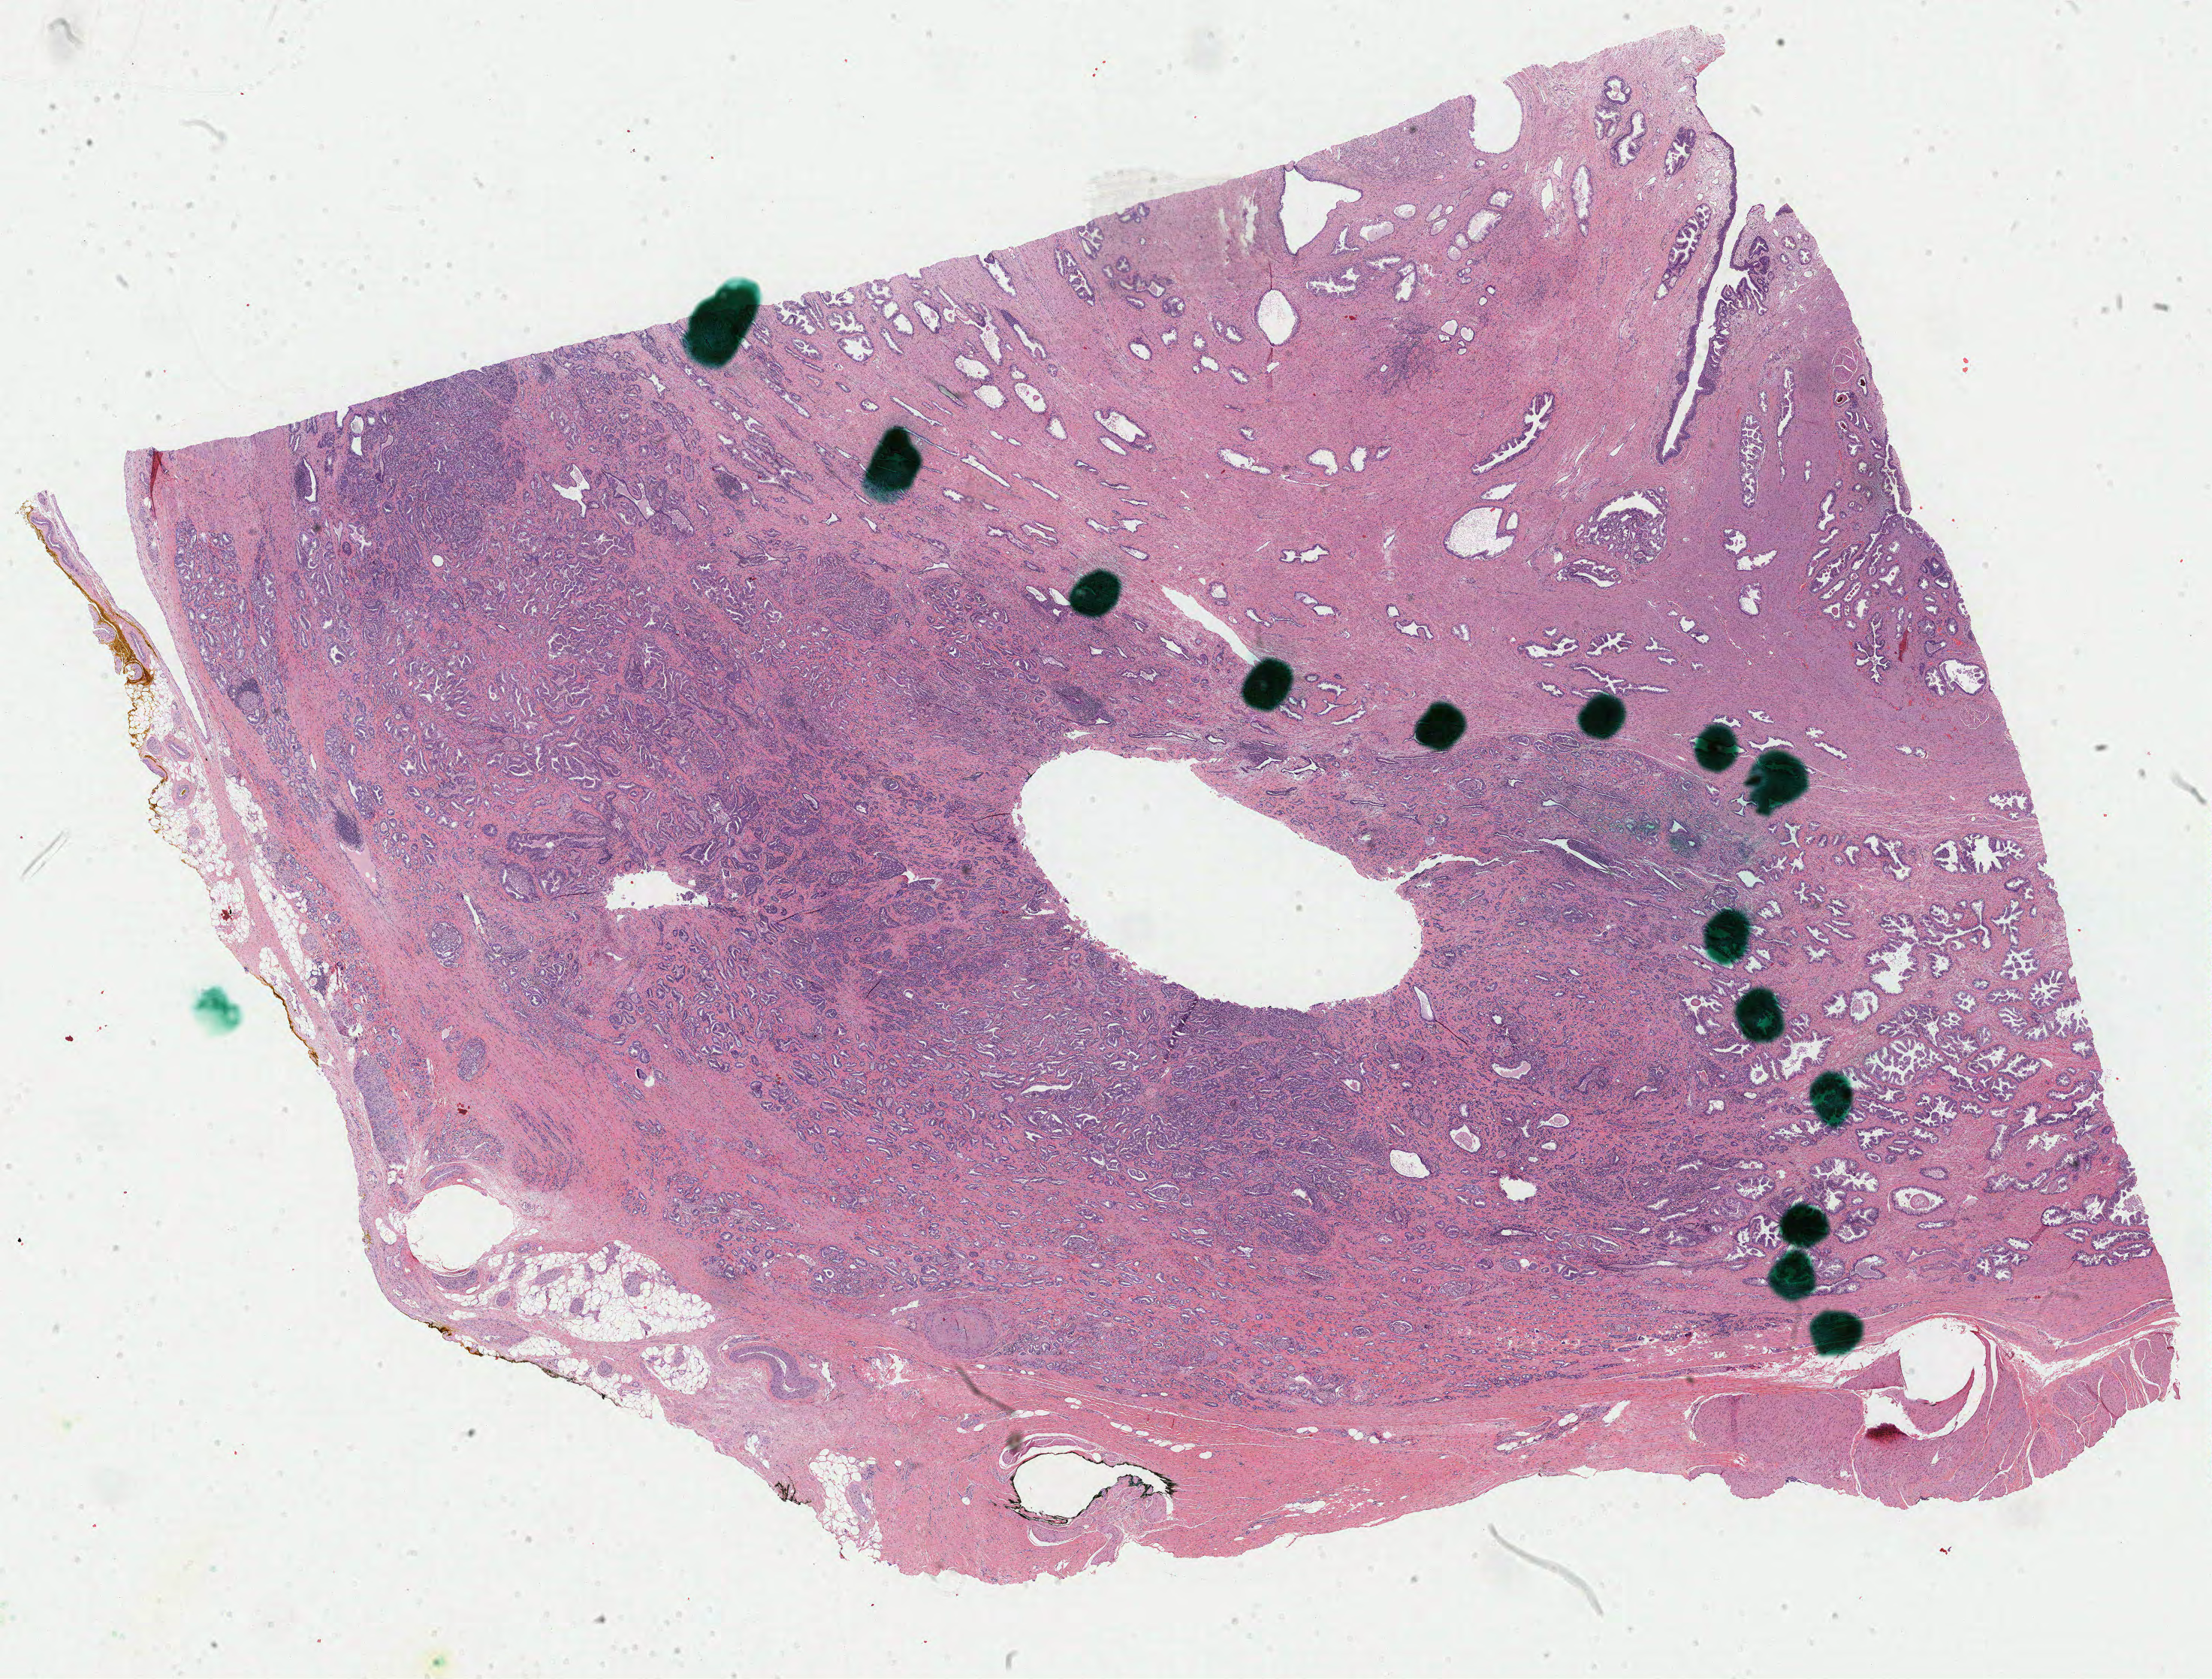
Hematoxylin and eosin (H&E) stained whole-slide image, low-resolution overview of the scanned area, about 23.4 x 17.7 mm (from a 40x scan), formalin-fixed paraffin-embedded (FFPE) diagnostic section, primary tumour sample from the prostate. Male patient; age at initial diagnosis 57 years.
Histologic diagnosis: Adenocarcinoma, NOS (prostate gland).